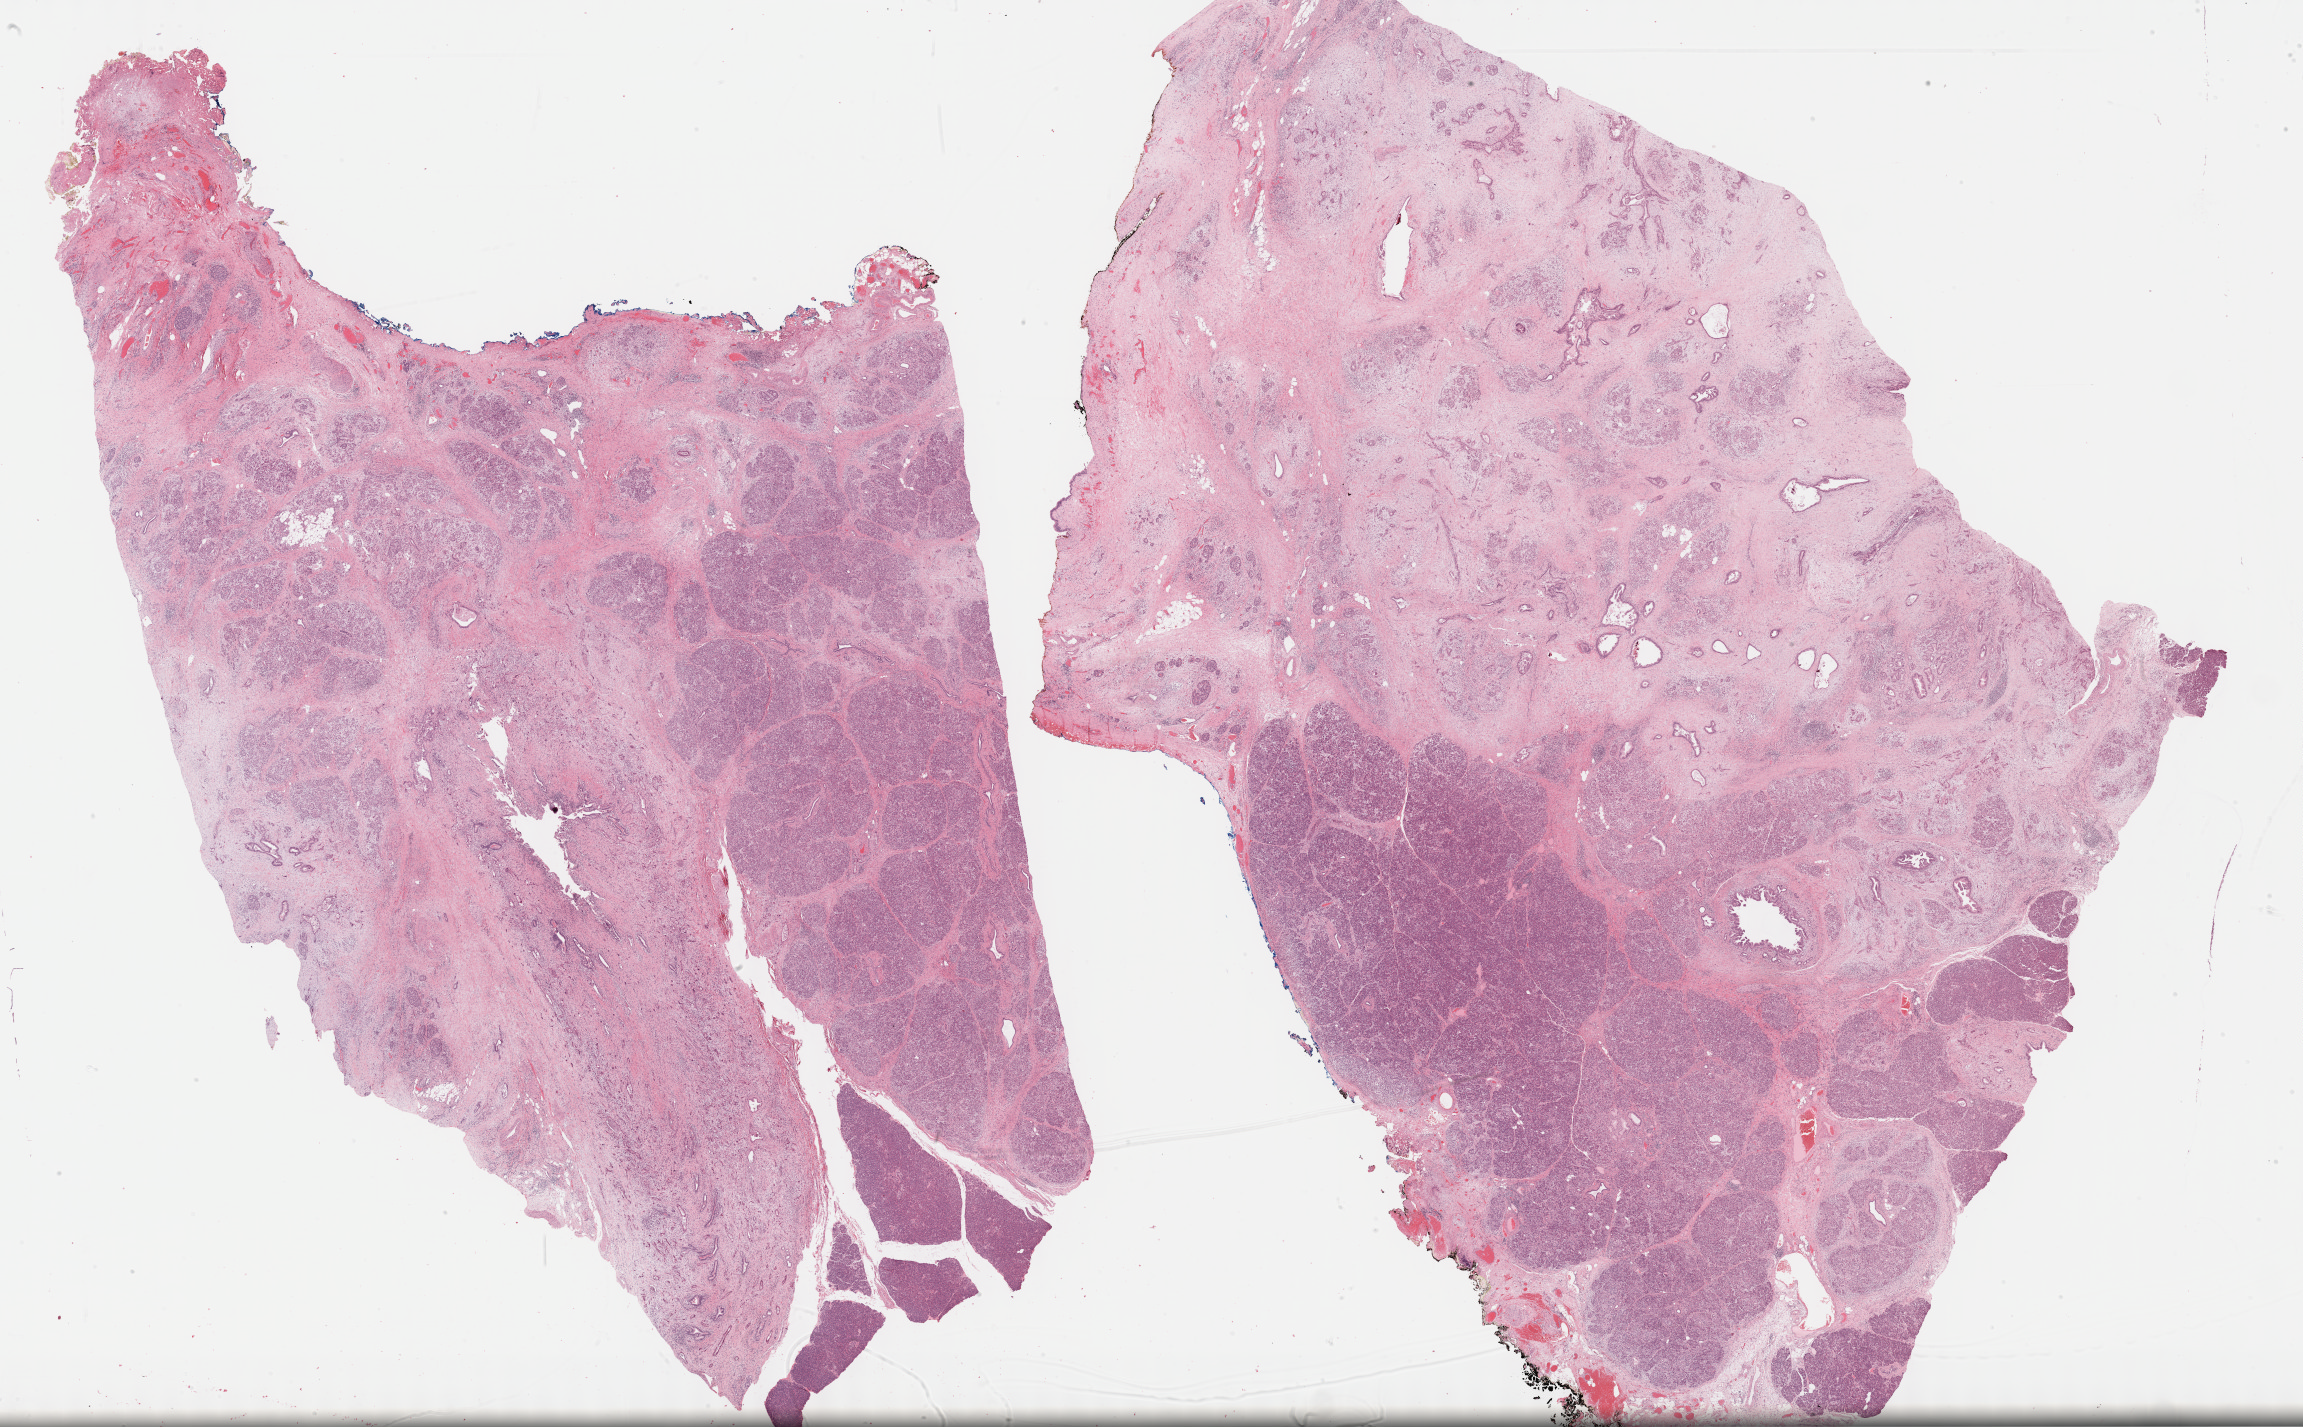
Hematoxylin and eosin (H&E) stained whole-slide image — whole scanned area (about 37.2 x 23.1 mm) shown as a low-resolution overview, formalin-fixed paraffin-embedded (FFPE) diagnostic section, pancreas, primary tumour sample. Patient: female, age at initial diagnosis 53 years. Histologic grade: G2 (moderately differentiated).
Diagnosis: Infiltrating duct carcinoma, NOS. Lymph nodes positive (case pathology): 2 of 17 examined. AJCC pathologic stage: IIB (6th edition).